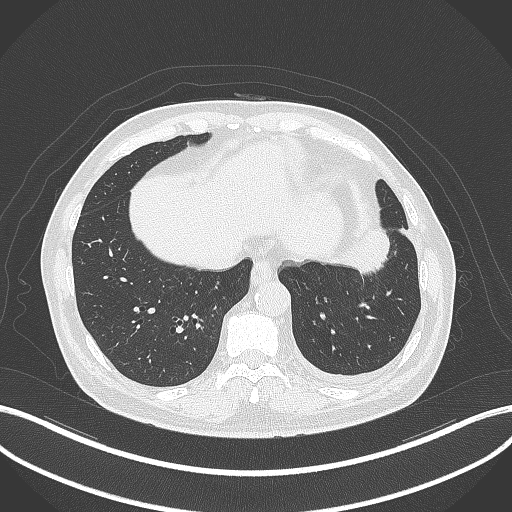
Chest CT, one axial slice; position 89 of 230 along the scan axis; 120 kVp; lung window (W 1500 / L -600 HU); 1 mm slice thickness; 512 × 512 image matrix, field of view 400 × 400 mm. Male patient, age 68 years. Case-level facts recorded for this patient, not image findings: clinical TNM (as recorded): T2b N0 M0.
Annotated regions visible in this slice (rectangle marked by the reading radiologist):
- lung tumour (recorded histology: squamous cell carcinoma): bounding box (x1, y1, x2, y2) in pixels: (348, 221, 396, 275)